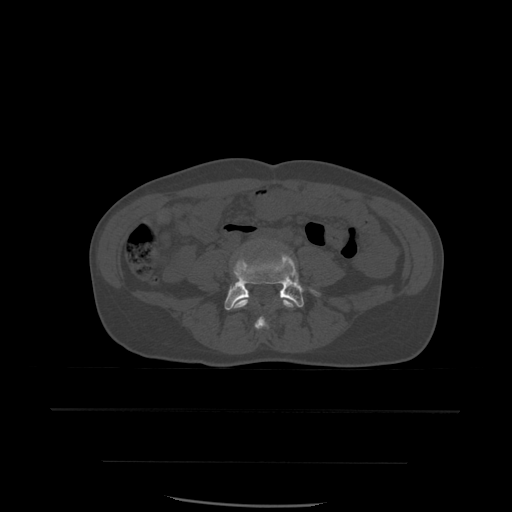
CT including the spine, one axial slice; position 157 of 574 along the scan axis; bone window (W 1800 / L 400 HU); 512 × 512 image matrix, field of view 392 × 392 mm. Patient age 48 years. Case-level facts recorded for this patient, not image findings: primary cancer: lung; vertebrae with lytic lesions (as recorded): T11.
Structures marked on this image (semi-automatic segmentation, software-assisted and operator-edited):
- L4 vertebra: bounding box [x1, y1, x2, y2] px = [232, 293, 297, 330]
- L5 vertebra: [225, 254, 320, 310]